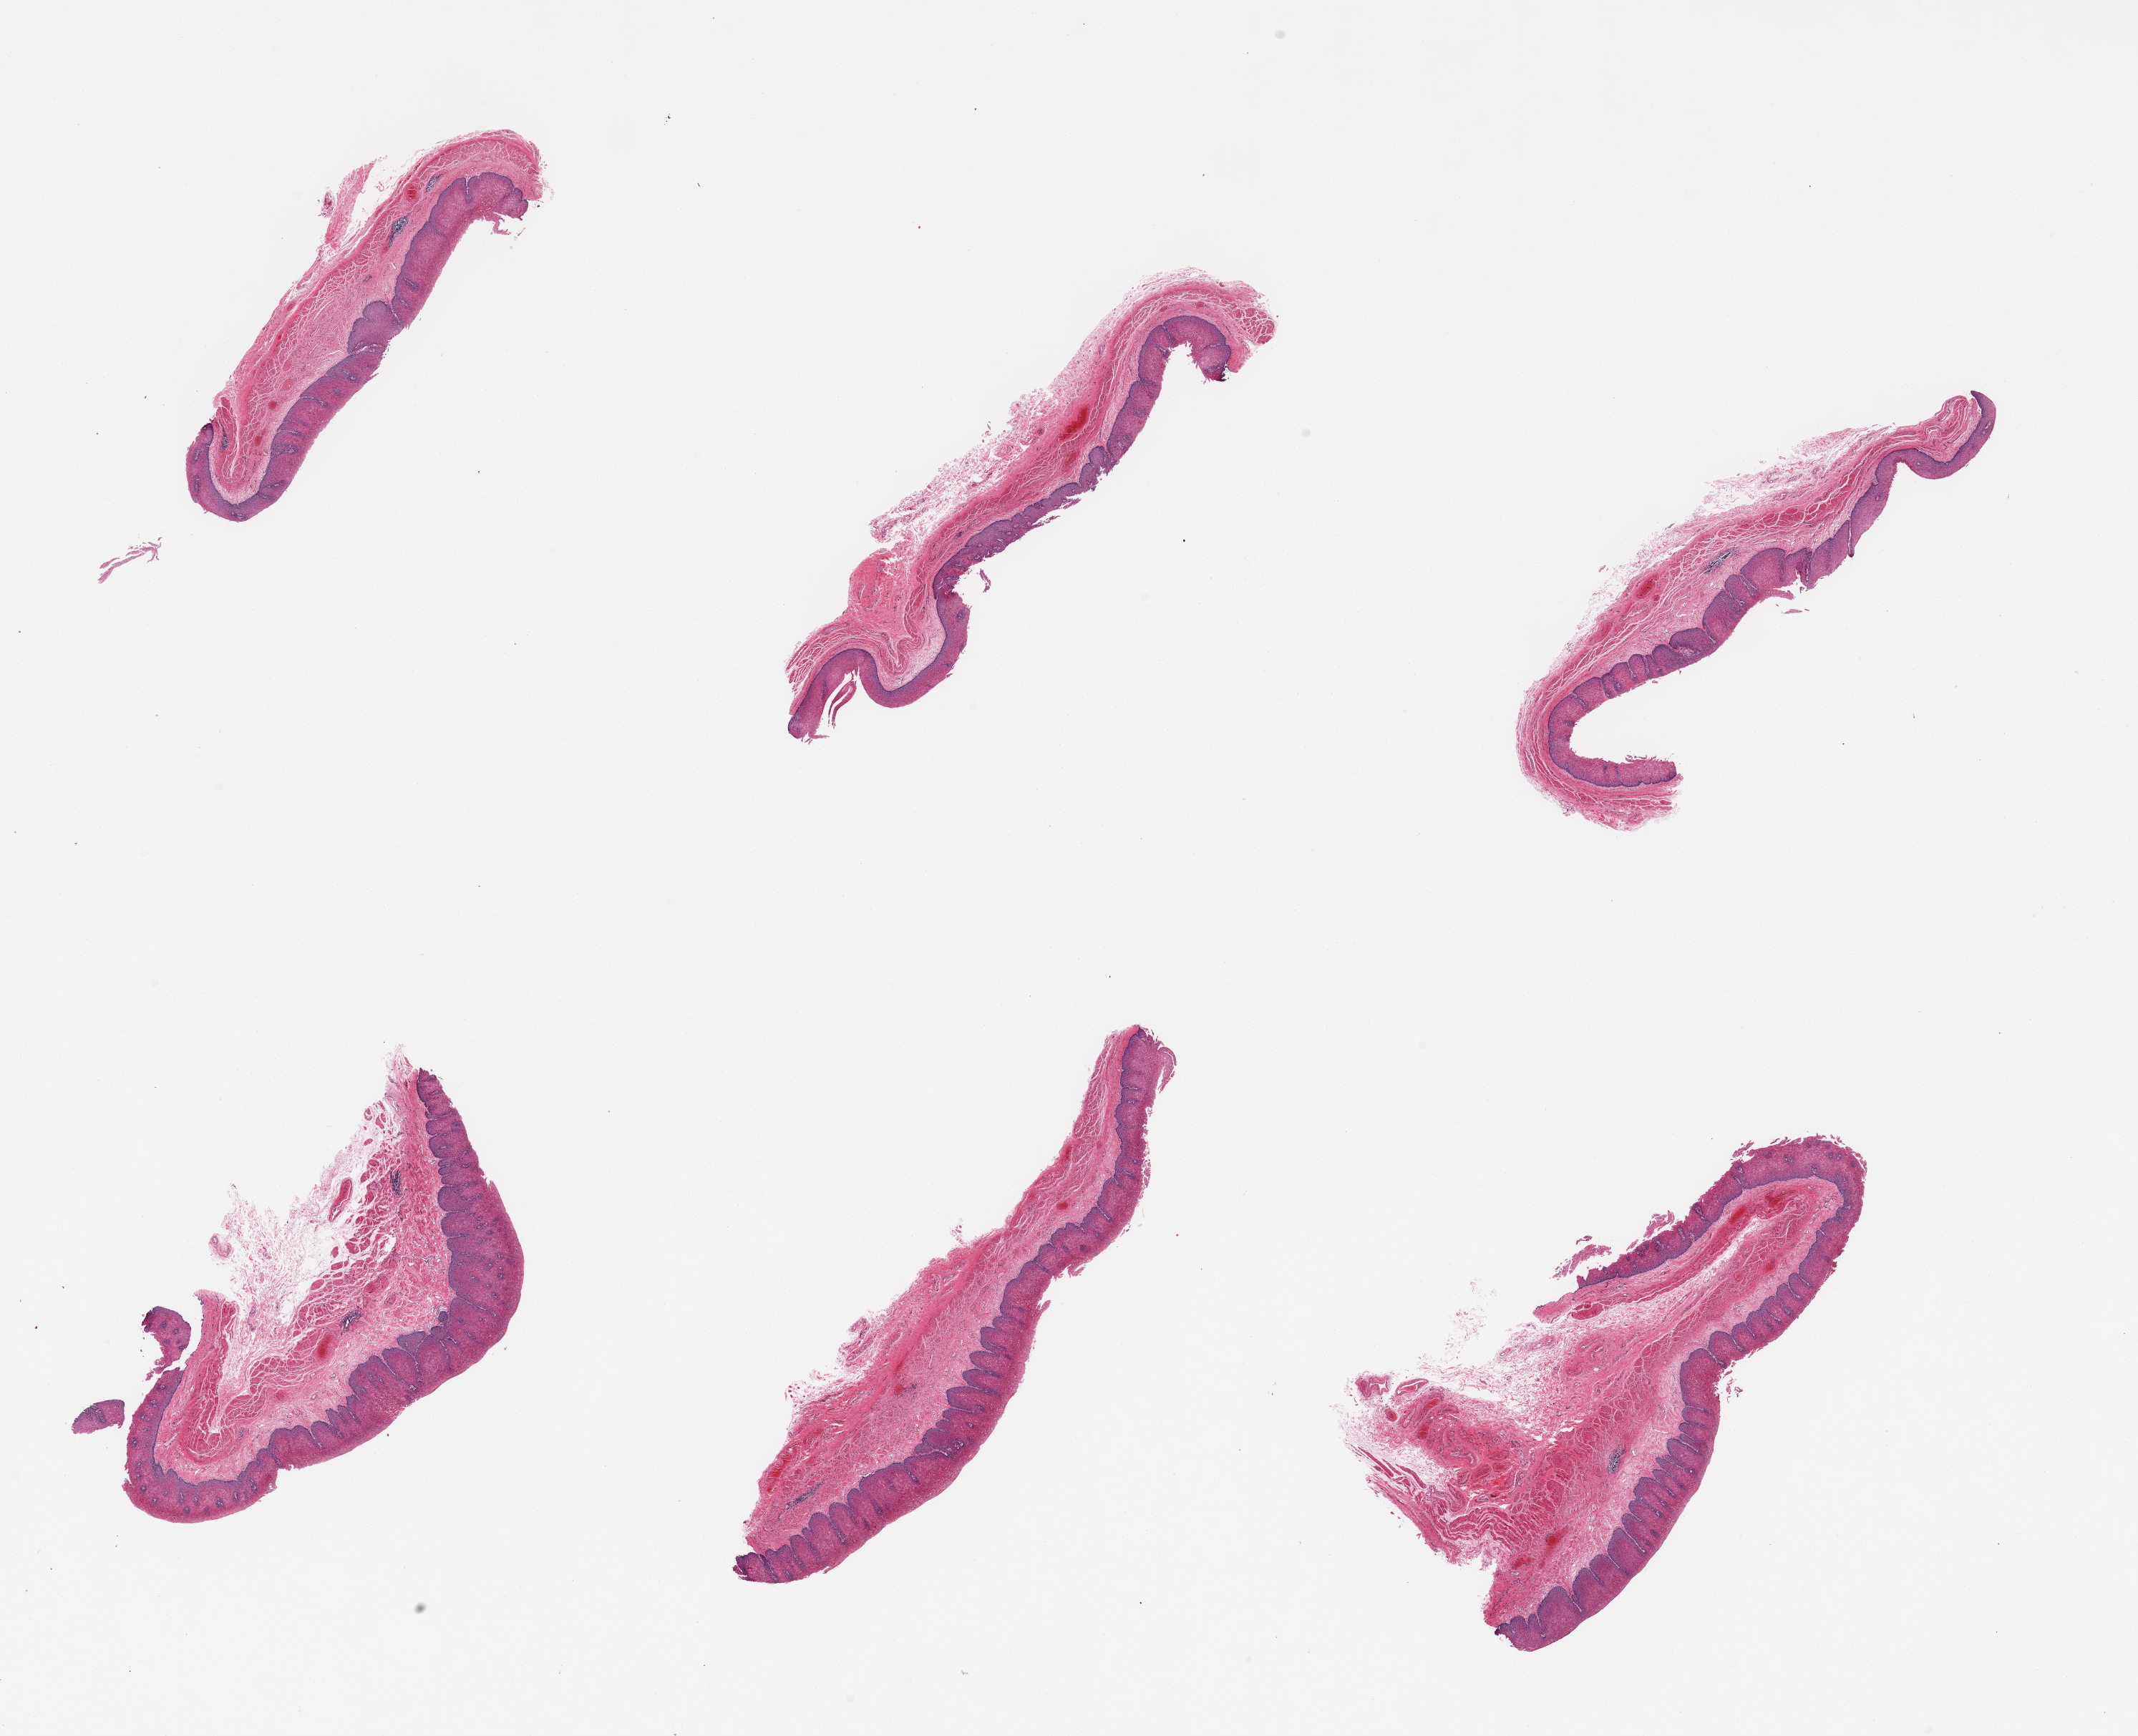
H&E whole-slide image, brightfield — whole scanned area (about 23.6 x 19.2 mm, acquisition: 20x scan) shown as a low-resolution overview. PAXgene-fixed, paraffin-embedded tissue. Sampled site (target tissue): esophageal mucous membrane. Tissue donor sample.
Review note (as recorded): 6 pieces, squamous mucosa up to ~0.8mm, 25-30% thickness.